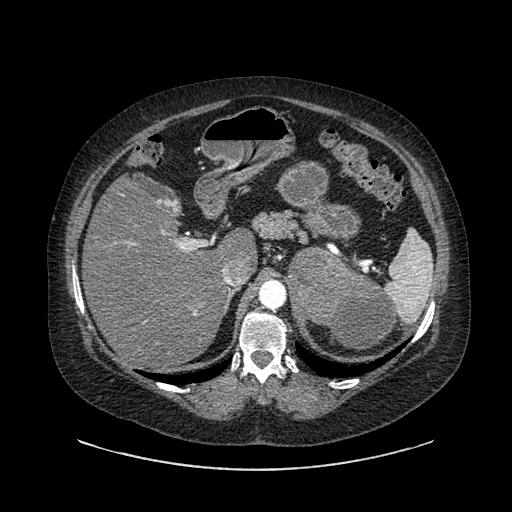
Contrast-enhanced abdominal CT, one axial slice. Slice 601 of 769 in the series (ordered by position). Reconstruction kernel SOFT. Intravenous contrast given. Soft-tissue window (W 400 / L 40 HU). 0.62 mm slice thickness. 512 × 512 image matrix. Female patient, age 61 years. Case-level facts recorded for this patient, not image findings: diagnosis: adrenocortical carcinoma; tumour side: left adrenal; tumour size at pathology: 13 cm; Ki-67 index: 79 %; stage (as recorded): 2.
Structures marked on this image (semi-automatically segmented with operator editing):
- mass: box from (x=289, y=250) to (x=395, y=351) px